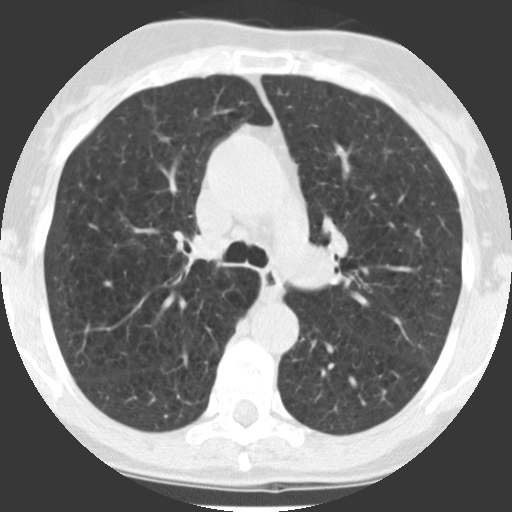
Axial slice from a low-dose chest CT screening exam, baseline annual screen, lung window (W 1500 / L -600 HU), standard (soft-tissue) reconstruction kernel (STANDARD), 120 kVp, slice 75 of 238 in the series, 512 × 512 image matrix, field of view 280 × 280 mm. Female, age 71 years at enrolment. Current smoker at enrolment.
Expert-annotated lung lesion, bounding box [x1, y1, x2, y2] px = [317, 331, 349, 362]. Screening reader's record for this exam: no non-calcified nodule ≥4 mm recorded.